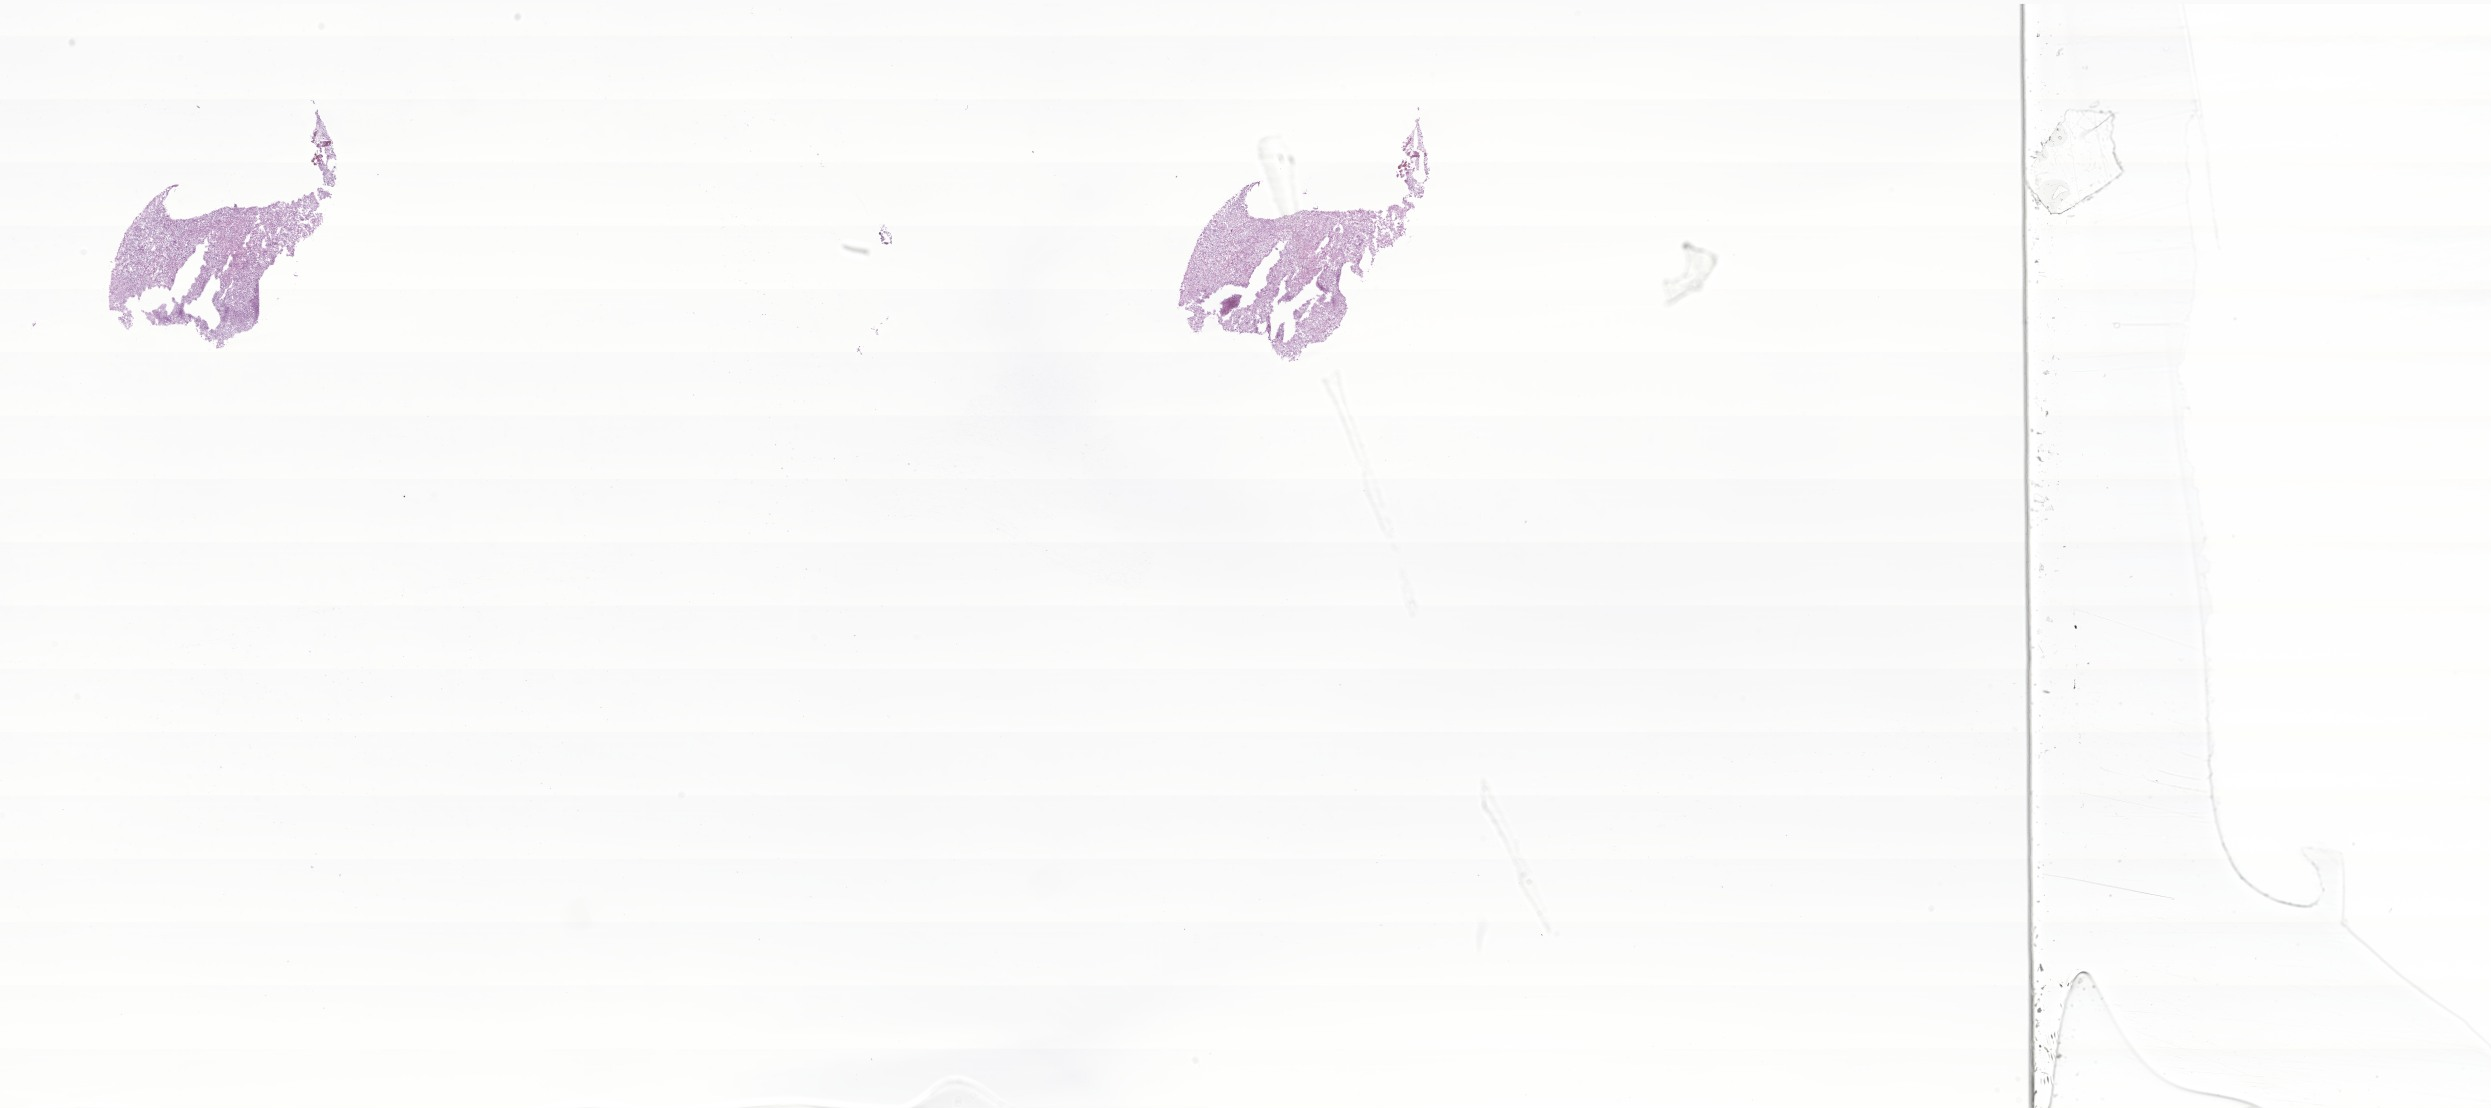
Whole-slide image, hematoxylin and eosin (H&E) stain of tumor tissue from the brain — shown as a low-resolution overview of the whole scanned area (about 42.0 x 18.7 mm), frozen section. Patient: female, age 167 months.
Recorded diagnosis: Neoplasm, uncertain whether benign or malignant.